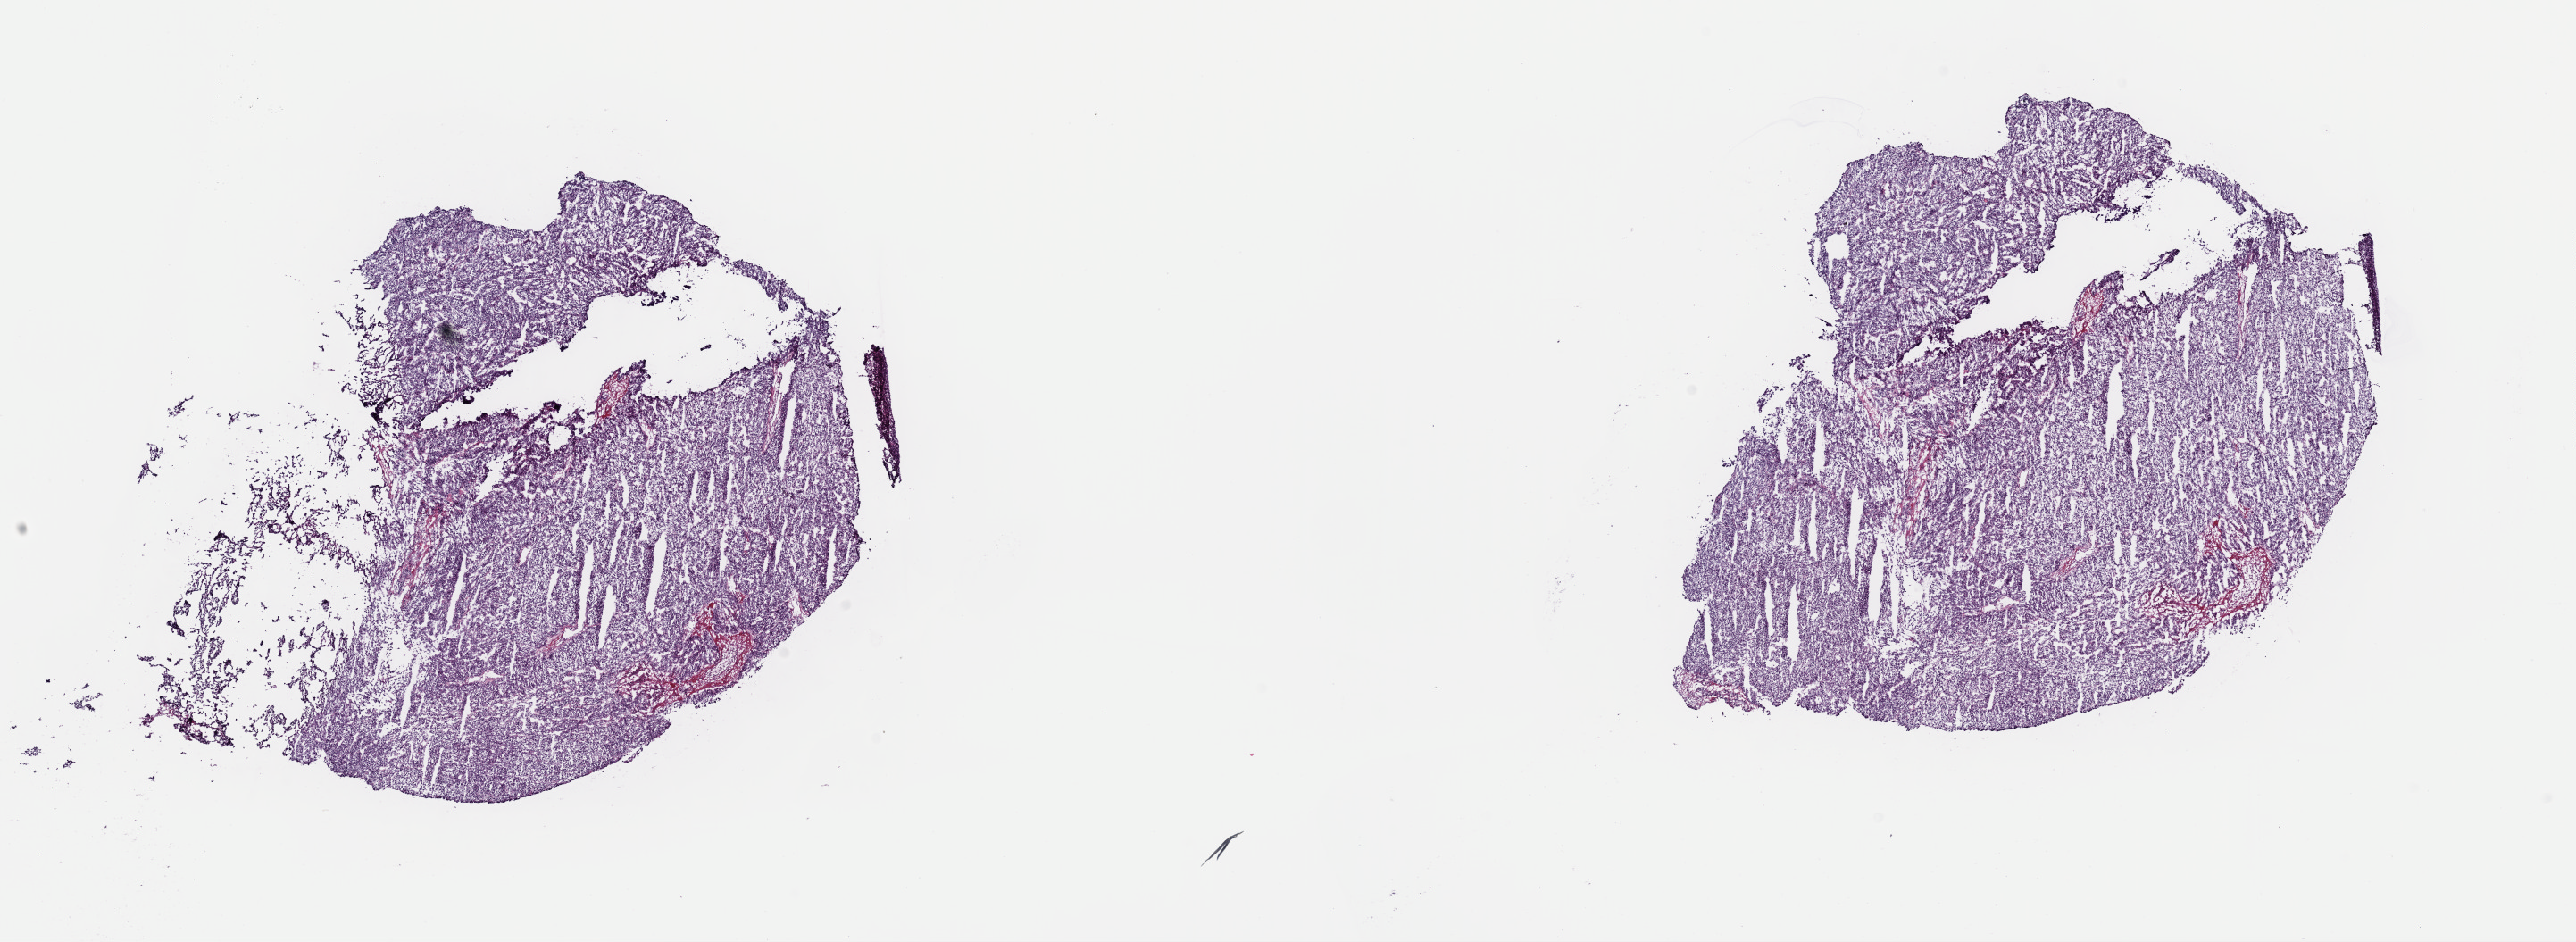
Whole-slide histology image, Hematoxylin and eosin (H&E) stained, a low-resolution overview of the entire scanned area, about 22.8 x 8.3 mm (slide scanned at 40x). Frozen section from the top of the tissue portion. Primary tumour sample from the liver. Patient: female, age at initial diagnosis 68 years. Histologic grade: G3 (poorly differentiated). Slide review estimates, as recorded: tumour cells 100%, tumour nuclei 95%, normal cells 0%, stromal cells 0%, necrosis 0%. Inflammatory infiltration, as recorded: lymphocyte infiltration 0%, monocyte infiltration 0%, neutrophil infiltration 0%.
Diagnosis: Hepatocellular carcinoma, NOS. AJCC pathologic stage: II (7th edition).